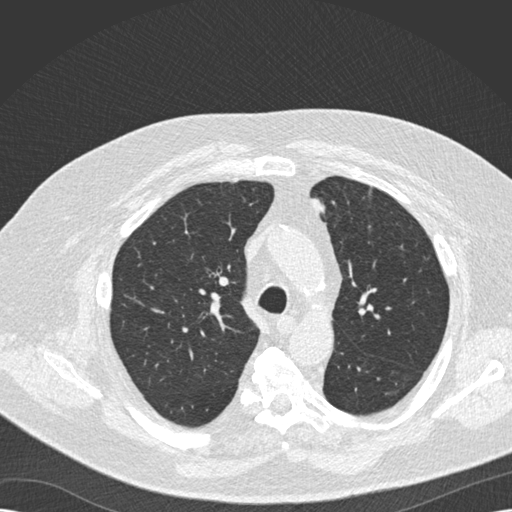
Low-dose screening chest CT, one axial slice; position 118 of 173 along the scan axis; reconstruction kernel B30f; 120 kVp; lung window (W 1500 / L -600 HU); 2 mm slice thickness; 512 × 512 image matrix, field of view 370 × 370 mm.
Structures marked on this image (manually delineated by an expert):
- lesion 1 (tumor, upper lobe of left lung): bounding box (x1, y1, x2, y2) in pixels: (313, 197, 325, 212)